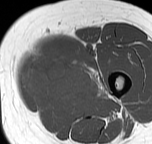
MRI of an extremity soft-tissue mass, one axial slice; MR volume resampled by the dataset authors to the PET/CT grid (not the native acquisition matrix); 152 × 144 image matrix, field of view 148 × 141 mm. Female patient. From the clinical record (not read from this slice): histological type: pleiomorphic leiomyosarcoma; grade: intermediate; site of the primary tumour: left thigh.
Annotated regions visible in this slice (expert contour drawn on MRI and transferred to this co-registered scan by the dataset authors):
- gross tumour volume including surrounding oedema: bounding box [x1, y1, x2, y2] px = [22, 49, 108, 105]
- gross tumour volume (mass): [24, 49, 99, 104]